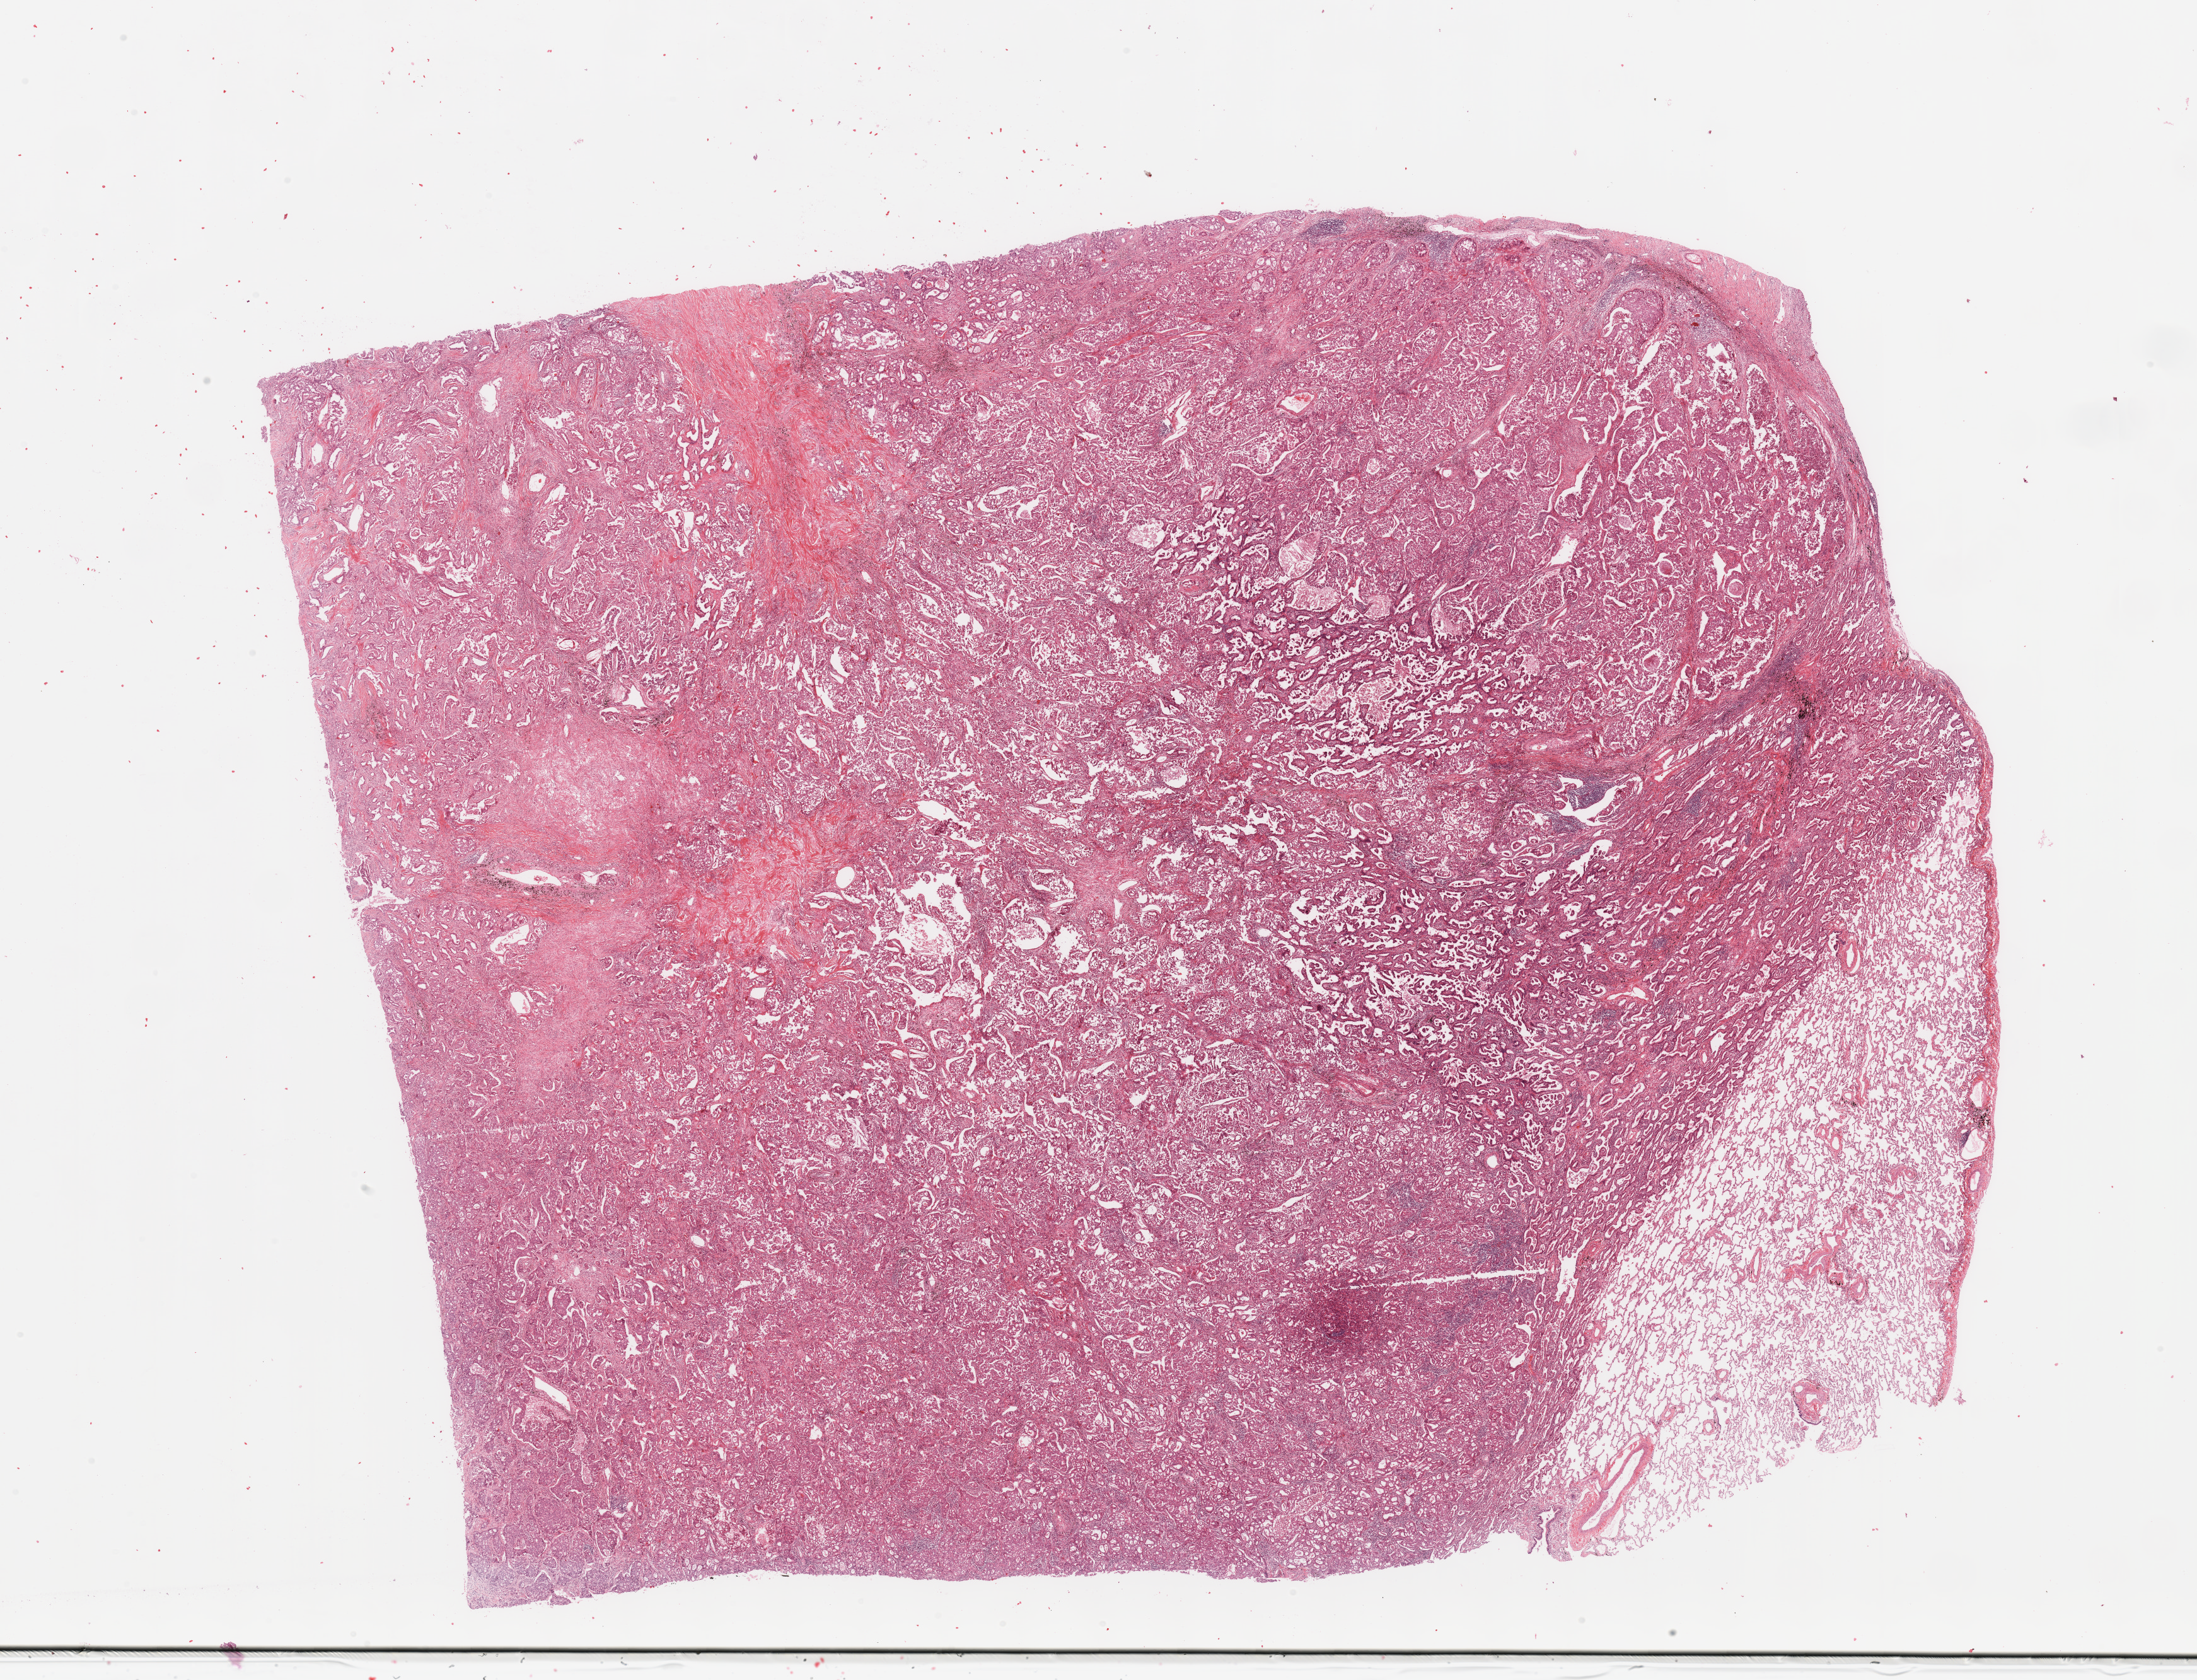
Digitized Hematoxylin and eosin (H&E) stained tissue section (whole slide), a low-resolution overview of the entire scanned area, about 27.6 x 21.1 mm, tumour tissue sample, lung. Patient: female, age 54 years. Histologic grade: G2 (moderately differentiated).
Diagnosis: Adenocarcinoma, NOS. AJCC pathologic stage: IIIA.